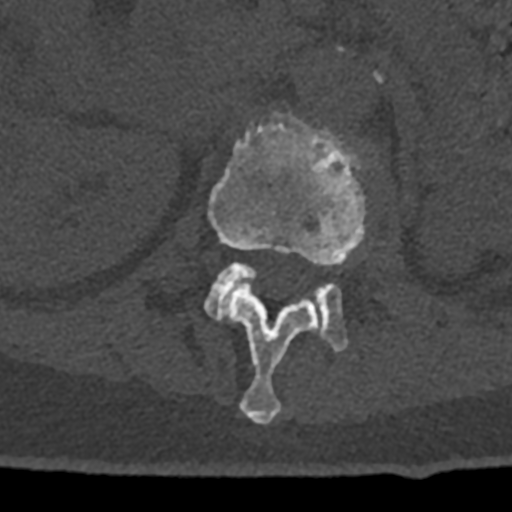
CT including the spine, one axial slice; position 414 of 797 along the scan axis; reconstruction kernel Br40s/3; 120 kVp; bone window (W 1800 / L 400 HU); 512 × 512 image matrix, field of view 160 × 160 mm. Male patient, age 74 years. From the clinical record (not read from this slice): primary cancer: renal; vertebrae with lytic lesions (as recorded): T10, L1, L2, L3, L4, L5.
Outlined on this slice (semi-automatic segmentation, software-assisted and operator-edited):
- L1 vertebra: bounding box <208,112,367,424> (left, top, right, bottom; pixels)
- L2 vertebra: <205,262,348,352>